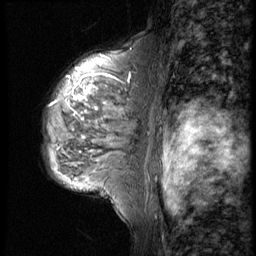
Breast MRI (dynamic contrast-enhanced), one sagittal slice; slice 35 of 56 in the series (ordered by position); 4 images stored at this slice position (order not interpretable as contrast timing); 1.5 T; TE 4.2 ms, TR 9 ms; 2.5 mm slice thickness; 256 × 256 image matrix. Female patient, age 50 years. From the clinical record (not read from this slice): setting: breast cancer imaged before/during neoadjuvant chemotherapy; receptor status: triple-negative.
Structures marked on this image (semi-automatically segmented with operator editing):
- analysis volume of interest (the breast-tissue region the enhancement analysis was run in; not a lesion): bounding box [x1, y1, x2, y2] px = [41, 46, 148, 188]
- tumour enhancement mask (voxels above the 140 % enhancement threshold inside the analysis volume of interest): [48, 79, 117, 107]